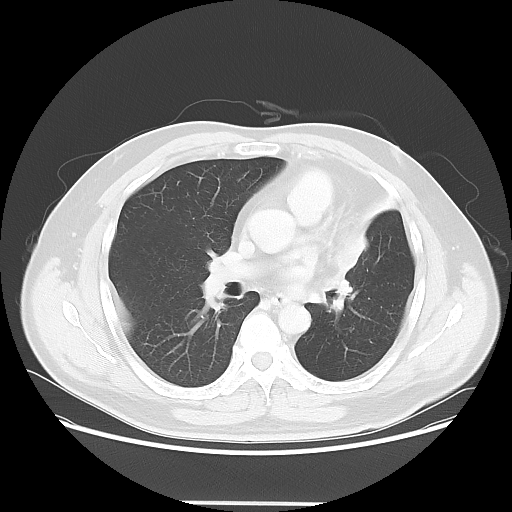
Chest CT, one axial slice. Position 34 of 62 along the scan axis. Lung window (W 1500 / L -600 HU). 5 mm slice thickness. 512 × 512 image matrix, field of view 403 × 403 mm. Patient: male, 49 years. Case-level facts recorded for this patient, not image findings: clinical TNM (as recorded): T3 N3 M1c.
Outlined on this slice (rectangle marked by the reading radiologist):
- lung tumour (recorded histology: squamous cell carcinoma): bounding box (x1, y1, x2, y2) in pixels: (322, 236, 383, 311)